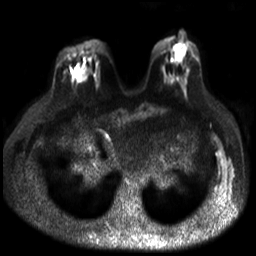
Breast MRI, one axial slice; slice 12 of 30 in the series (ordered by position); diffusion-weighted series; image 2 of 4 stored at this slice position (different b-values; order by instance number); 3 T; 4 mm slice thickness; 256 × 256 image matrix, field of view 320 × 320 mm. Female patient.
Outlined on this slice (outlined manually by an expert reader):
- tumour on diffusion-weighted imaging: bounding box [x1, y1, x2, y2] px = [73, 67, 83, 82]